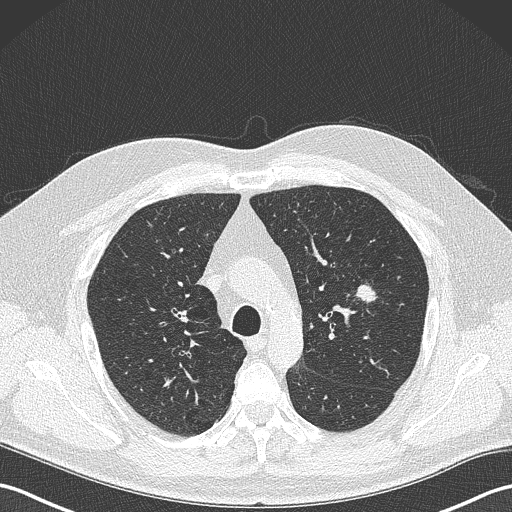
Low-dose screening chest CT, one axial slice. Position 244 of 343 along the scan axis. Lung window (W 1500 / L -600 HU). 512 × 512 image matrix, field of view 350 × 350 mm.
Annotated regions visible in this slice (expert manual segmentation):
- lesion 1 (tumor, upper lobe of left lung): bounding box (x1, y1, x2, y2) in pixels: (356, 283, 378, 304)